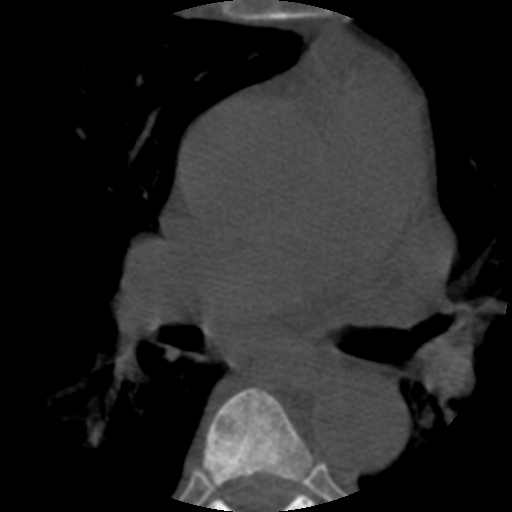
CT including the spine, one axial slice; reconstruction kernel STANDARD; bone window (W 1800 / L 400 HU); 1.25 mm slice thickness; 512 × 512 image matrix. Patient age 57 years. Case-level facts recorded for this patient, not image findings: primary cancer: prostate.
Annotated regions visible in this slice (semi-automatic segmentation, software-assisted and operator-edited):
- T5 vertebra: bounding box [x1, y1, x2, y2] px = [203, 387, 313, 490]
- T6 vertebra: [208, 482, 313, 512]